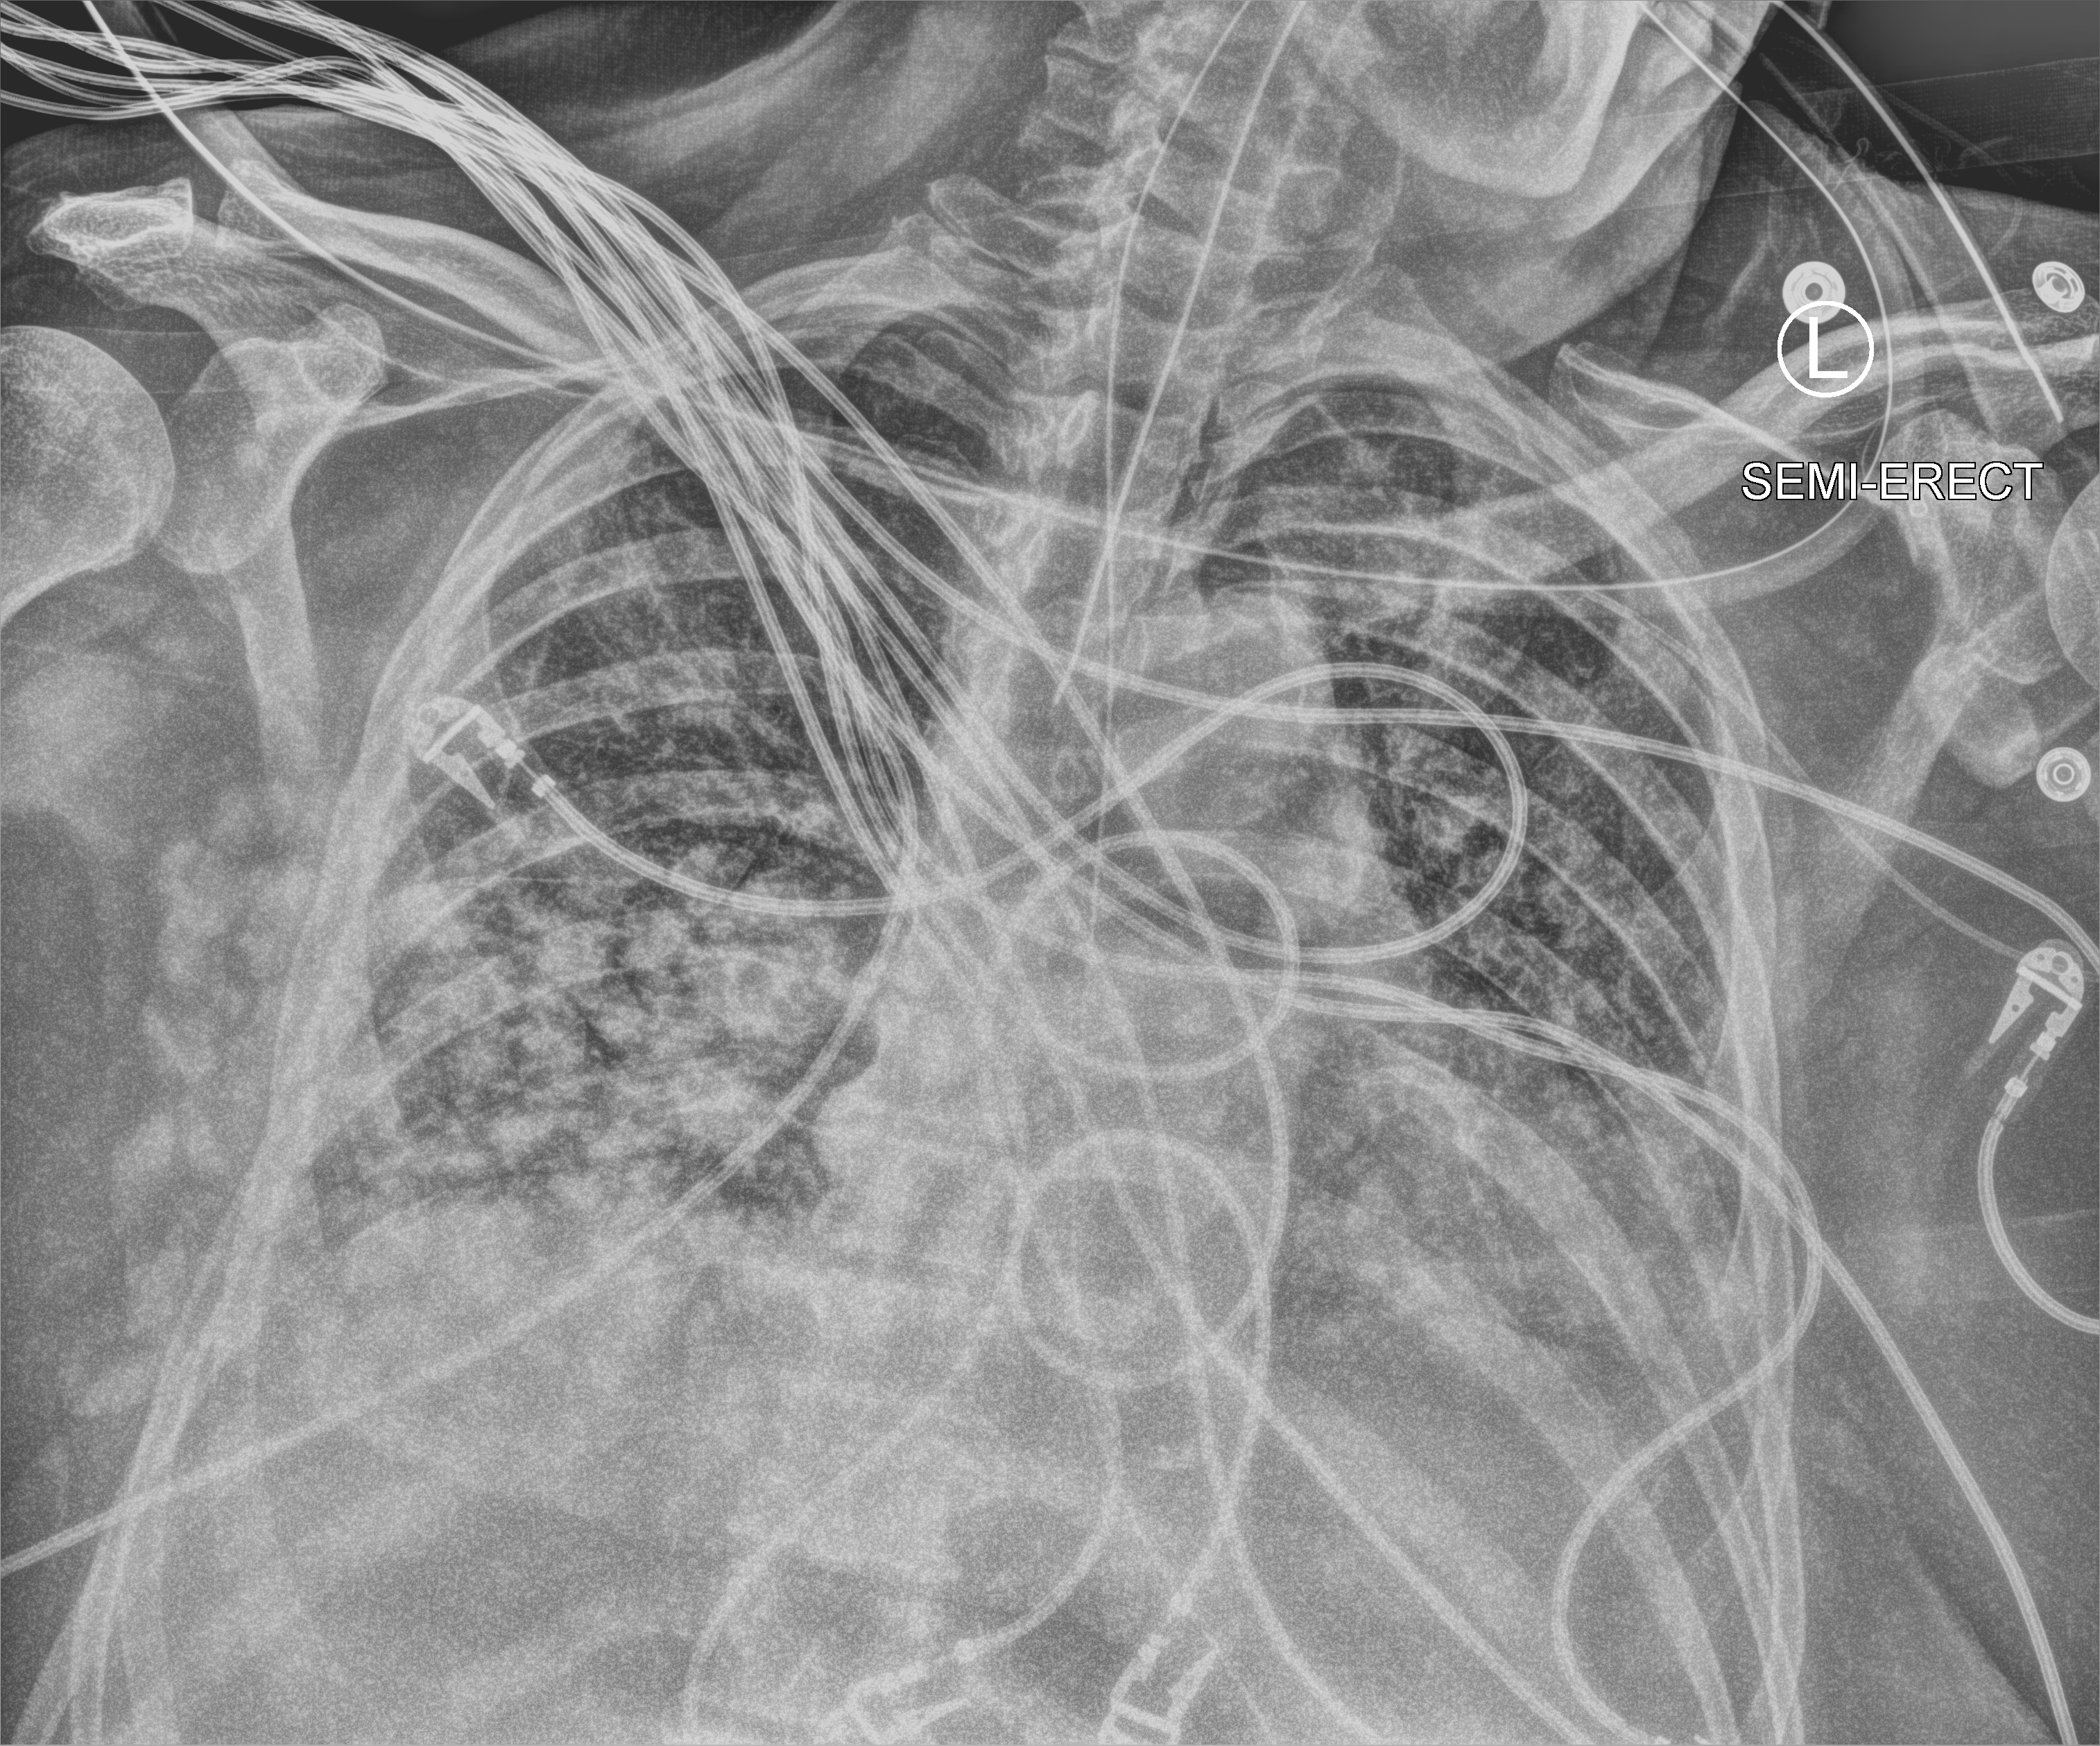
Bedside chest radiograph (computed radiography); anteroposterior (AP) projection. Male patient hospitalised with COVID-19, age 60–74 years.
From the hospital-stay record, not from the radiograph (when in the stay this image was taken is not recorded):
- mechanically ventilated during this hospital stay: yes
- admitted to intensive care during this hospital stay: yes